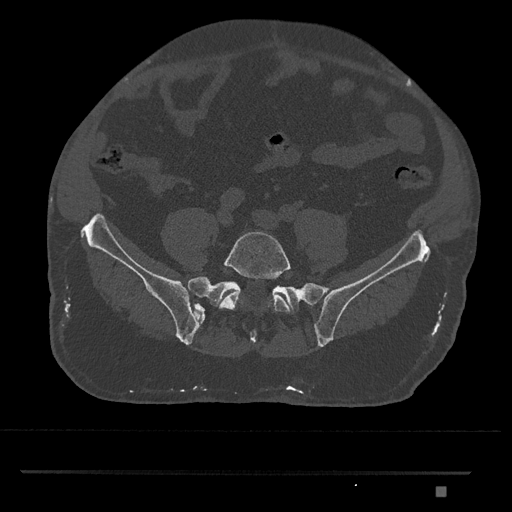
CT including the spine, one axial slice; slice 537 of 1134 in the series (ordered by position); reconstruction kernel Br40s/3; bone window (W 1800 / L 400 HU); 512 × 512 image matrix, field of view 429 × 429 mm. Male patient, age 65 years. Case-level facts recorded for this patient, not image findings: primary cancer: prostate.
Structures marked on this image (semi-automatic segmentation, software-assisted and operator-edited):
- L5 vertebra: bounding box (x1, y1, x2, y2) in pixels: (219, 231, 291, 314)